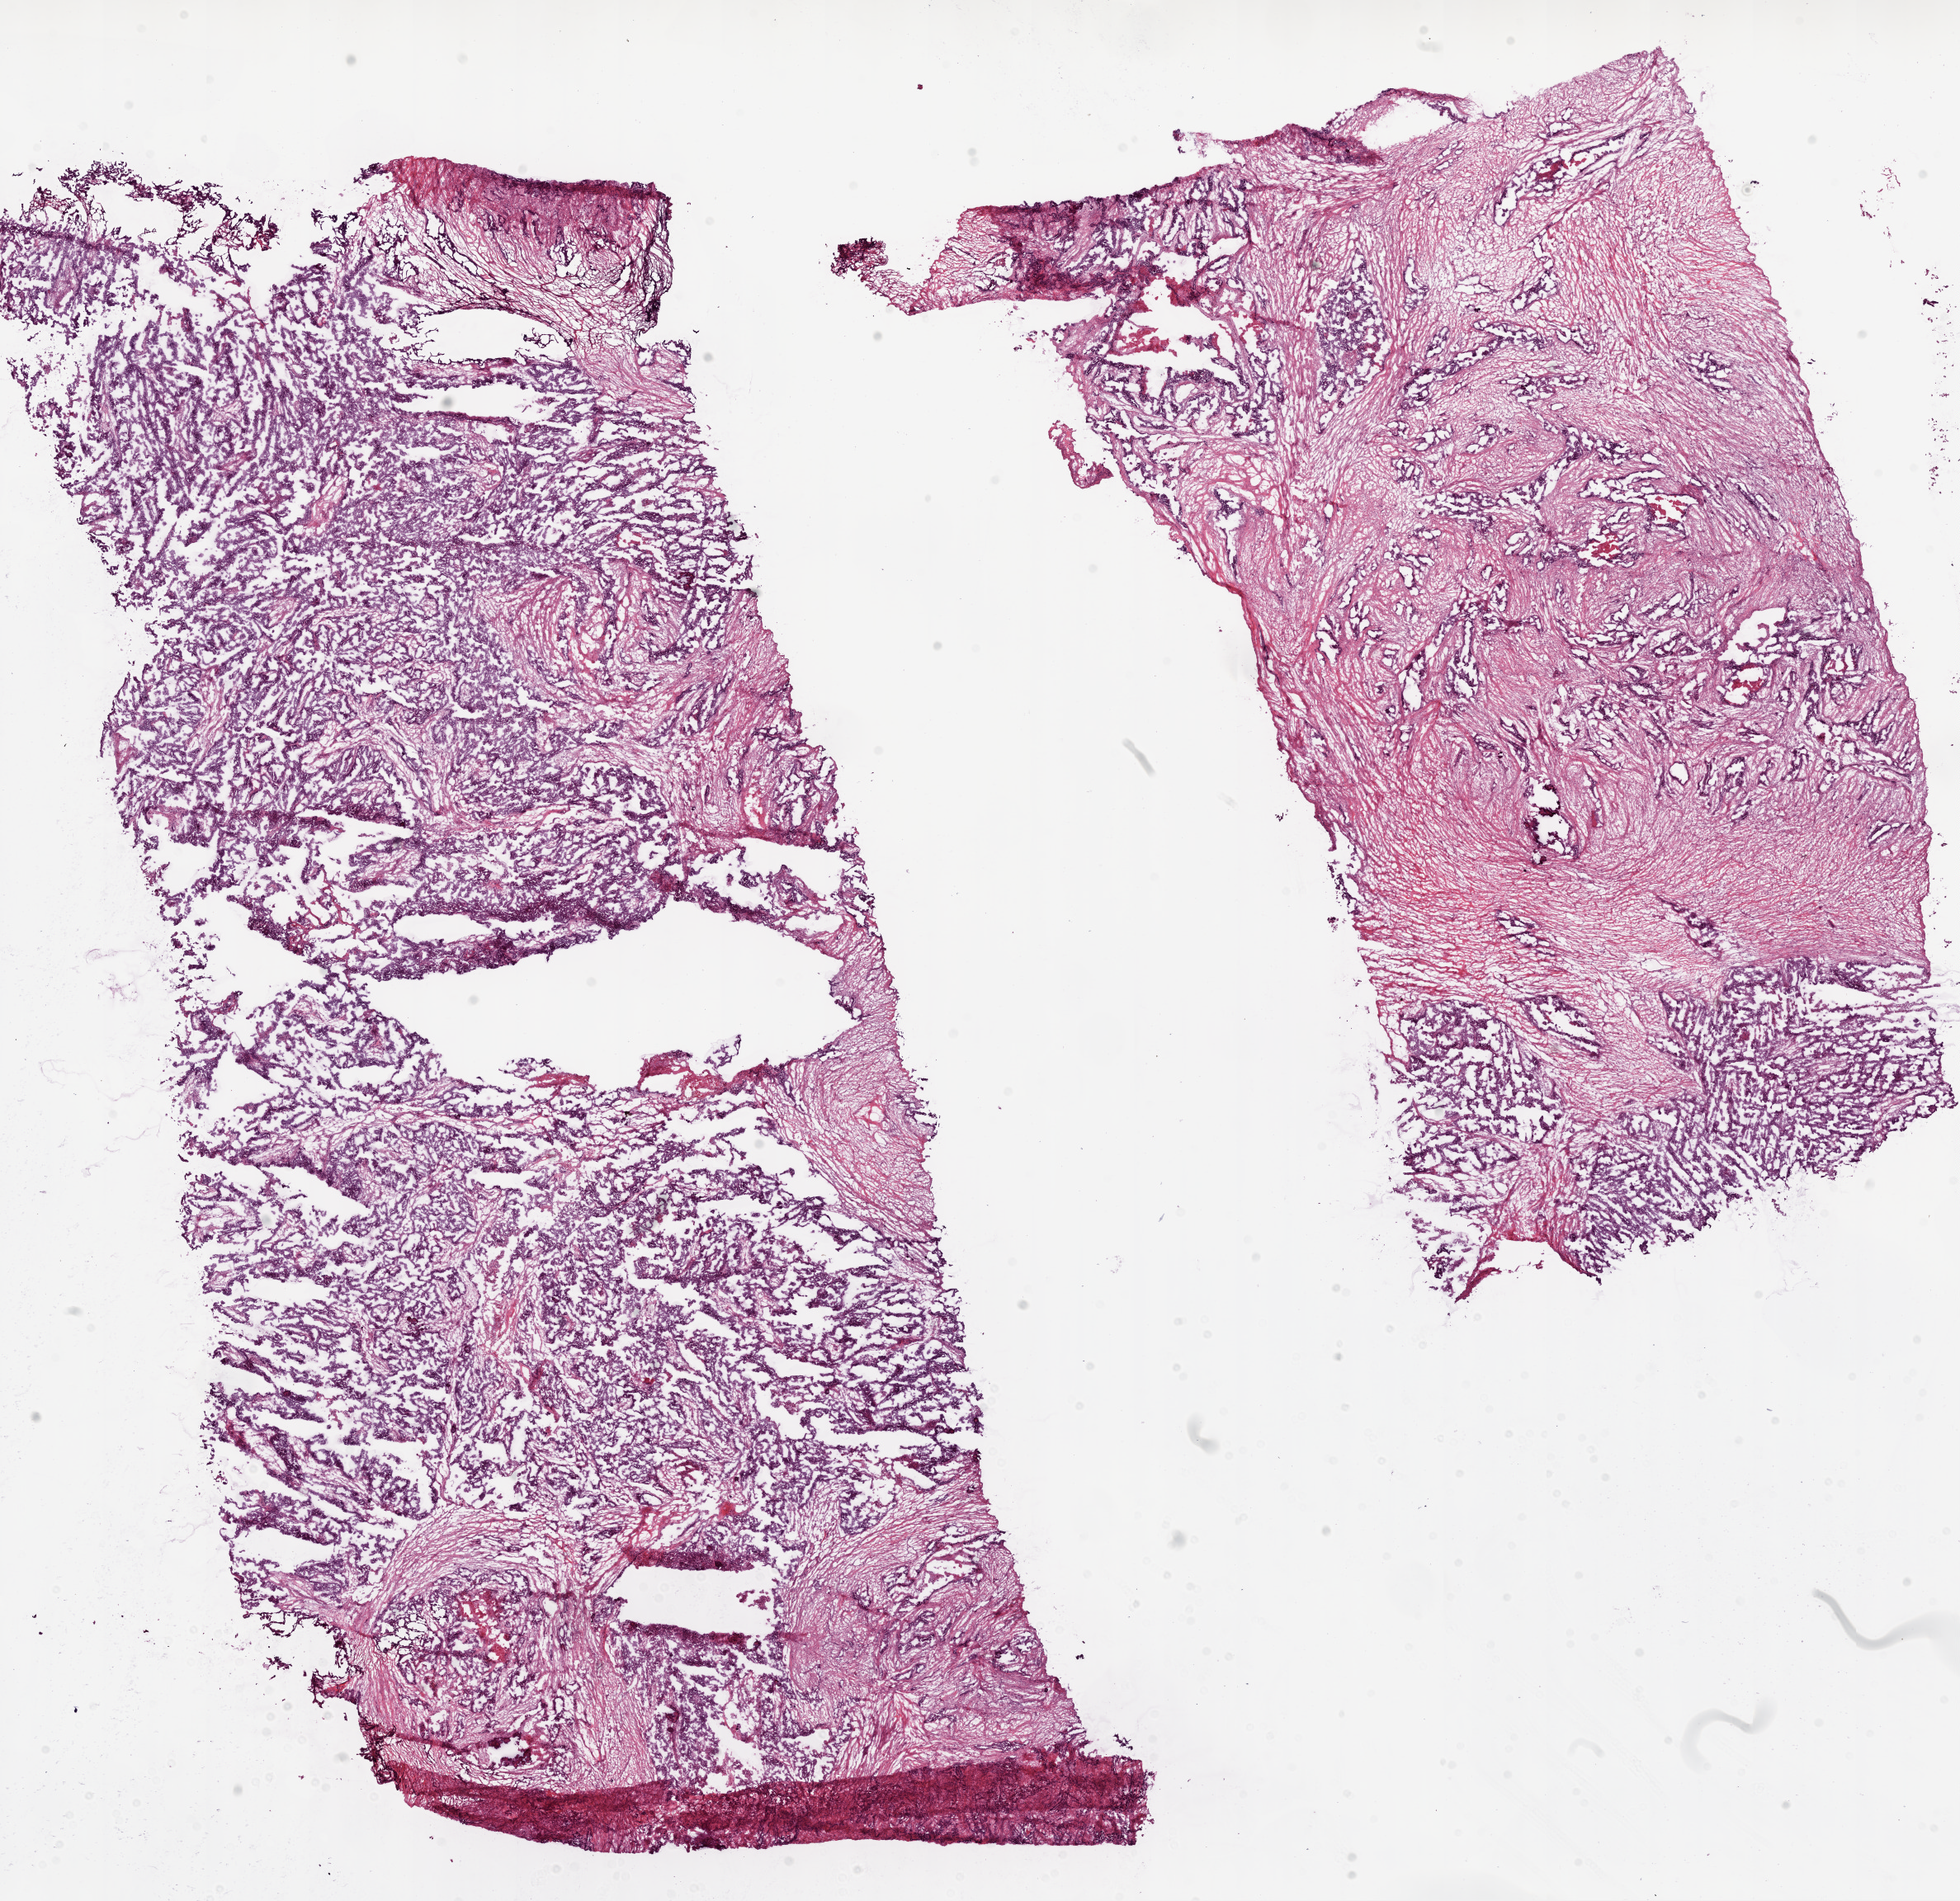
Whole-slide histology image, Hematoxylin and eosin (H&E) stained, shown as a low-resolution overview of the whole scanned area (about 19.1 x 18.5 mm). Frozen section from the bottom of the tissue portion. Primary tumour sample from the ovary. Female patient; age at initial diagnosis 60 years. Histologic grade: G2 (moderately differentiated). Composition of this section per pathologist review: tumour cells 79%, tumour nuclei 80%, normal cells 0%, stromal cells 20%, necrosis 1%.
FIGO stage: IIIC. Pathologic diagnosis: Serous cystadenocarcinoma, NOS.